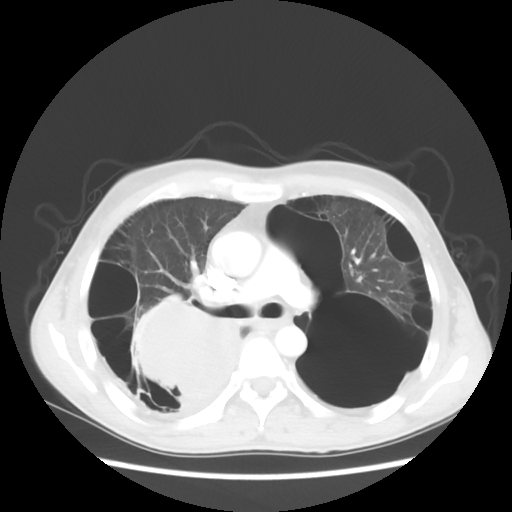
Chest CT, one axial slice; position 34 of 56 along the scan axis; 140 kVp; lung window (W 1500 / L -600 HU); 512 × 512 image matrix. Male patient, age 41 years. Case-level facts recorded for this patient, not image findings: clinical TNM (as recorded): T4 N0 M1a.
Structures marked on this image (rectangle marked by the reading radiologist):
- lung tumour (recorded histology: large cell carcinoma): bounding box (x1, y1, x2, y2) in pixels: (123, 293, 254, 414)